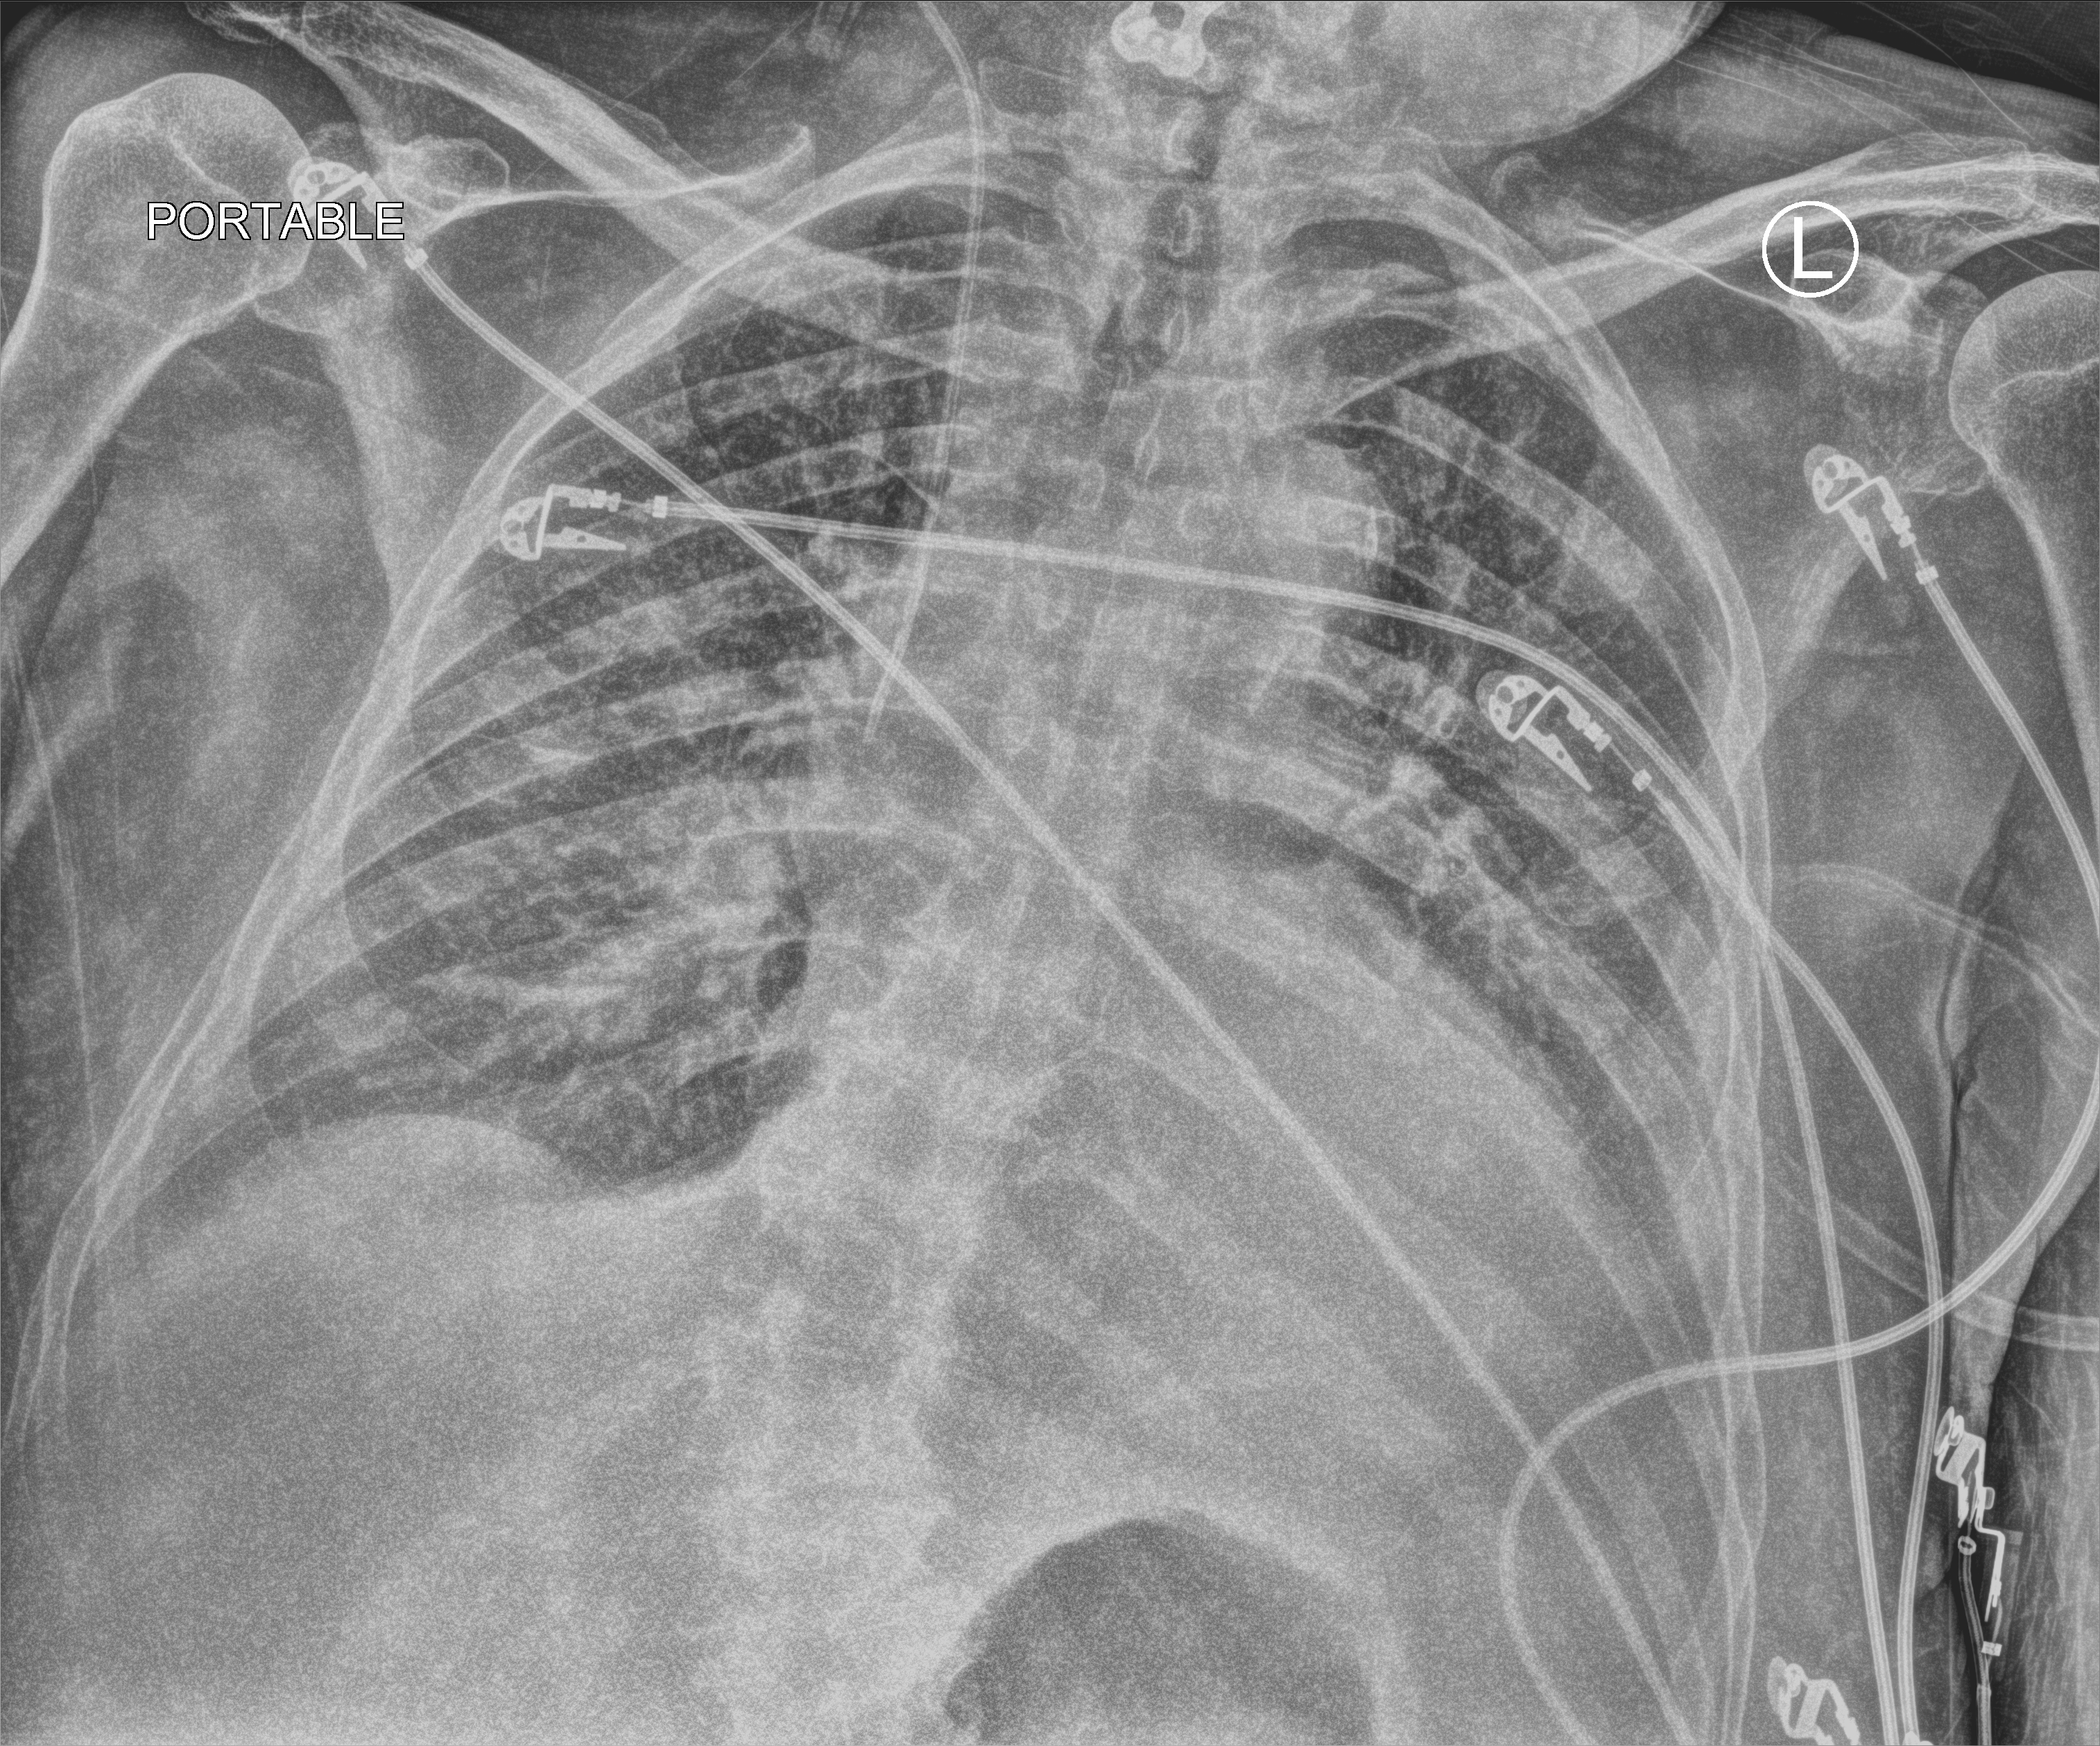
Bedside chest radiograph (computed radiography), anteroposterior (AP) projection. Male patient hospitalised with COVID-19, age 75–90 years.
Hospital-stay facts (about this admission, not read from this image; timing relative to this image not recorded): chronic kidney disease (admission record): no.